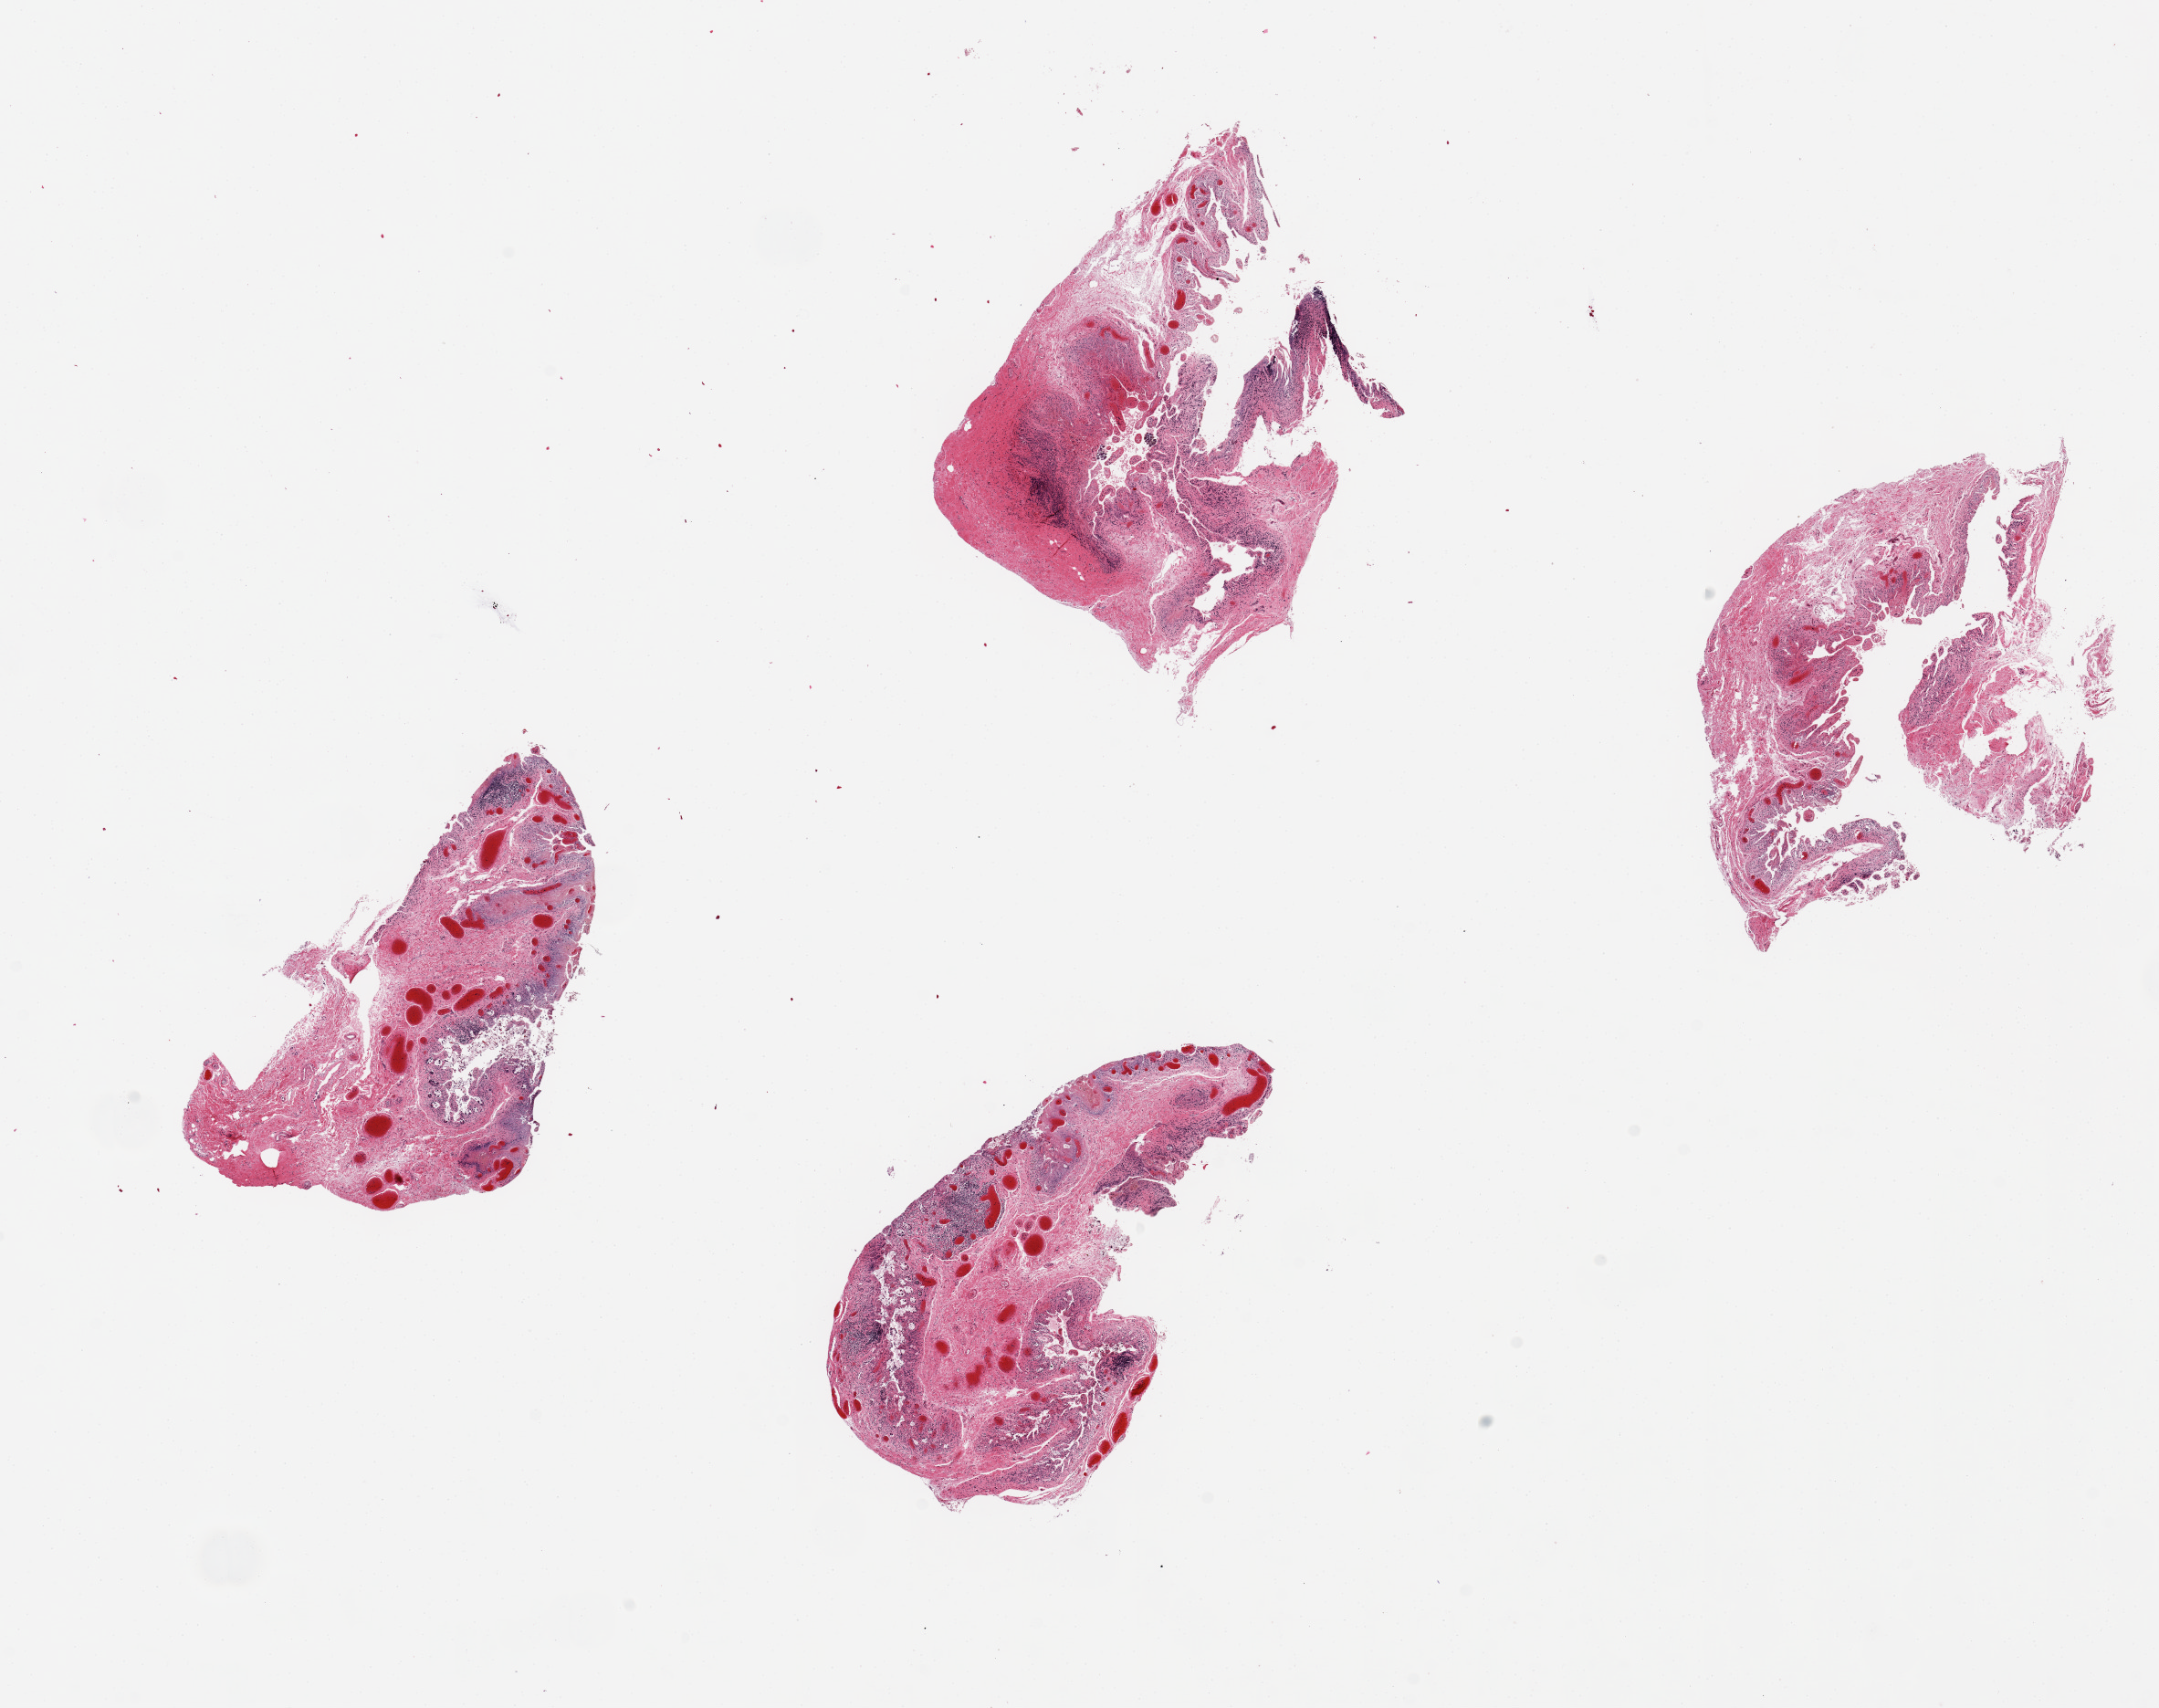
Whole-slide image, haematoxylin and eosin stain, low-resolution overview of the scanned area, about 18.7 x 14.8 mm (acquisition: 20x scan), PAXgene-fixed, paraffin-embedded tissue, section of ileum (target tissue), tissue donor sample. Male donor.
Review note (as recorded): 4 pieces up to 4x3mm; badly autolyzed. Lymphoid aggregates <5%.